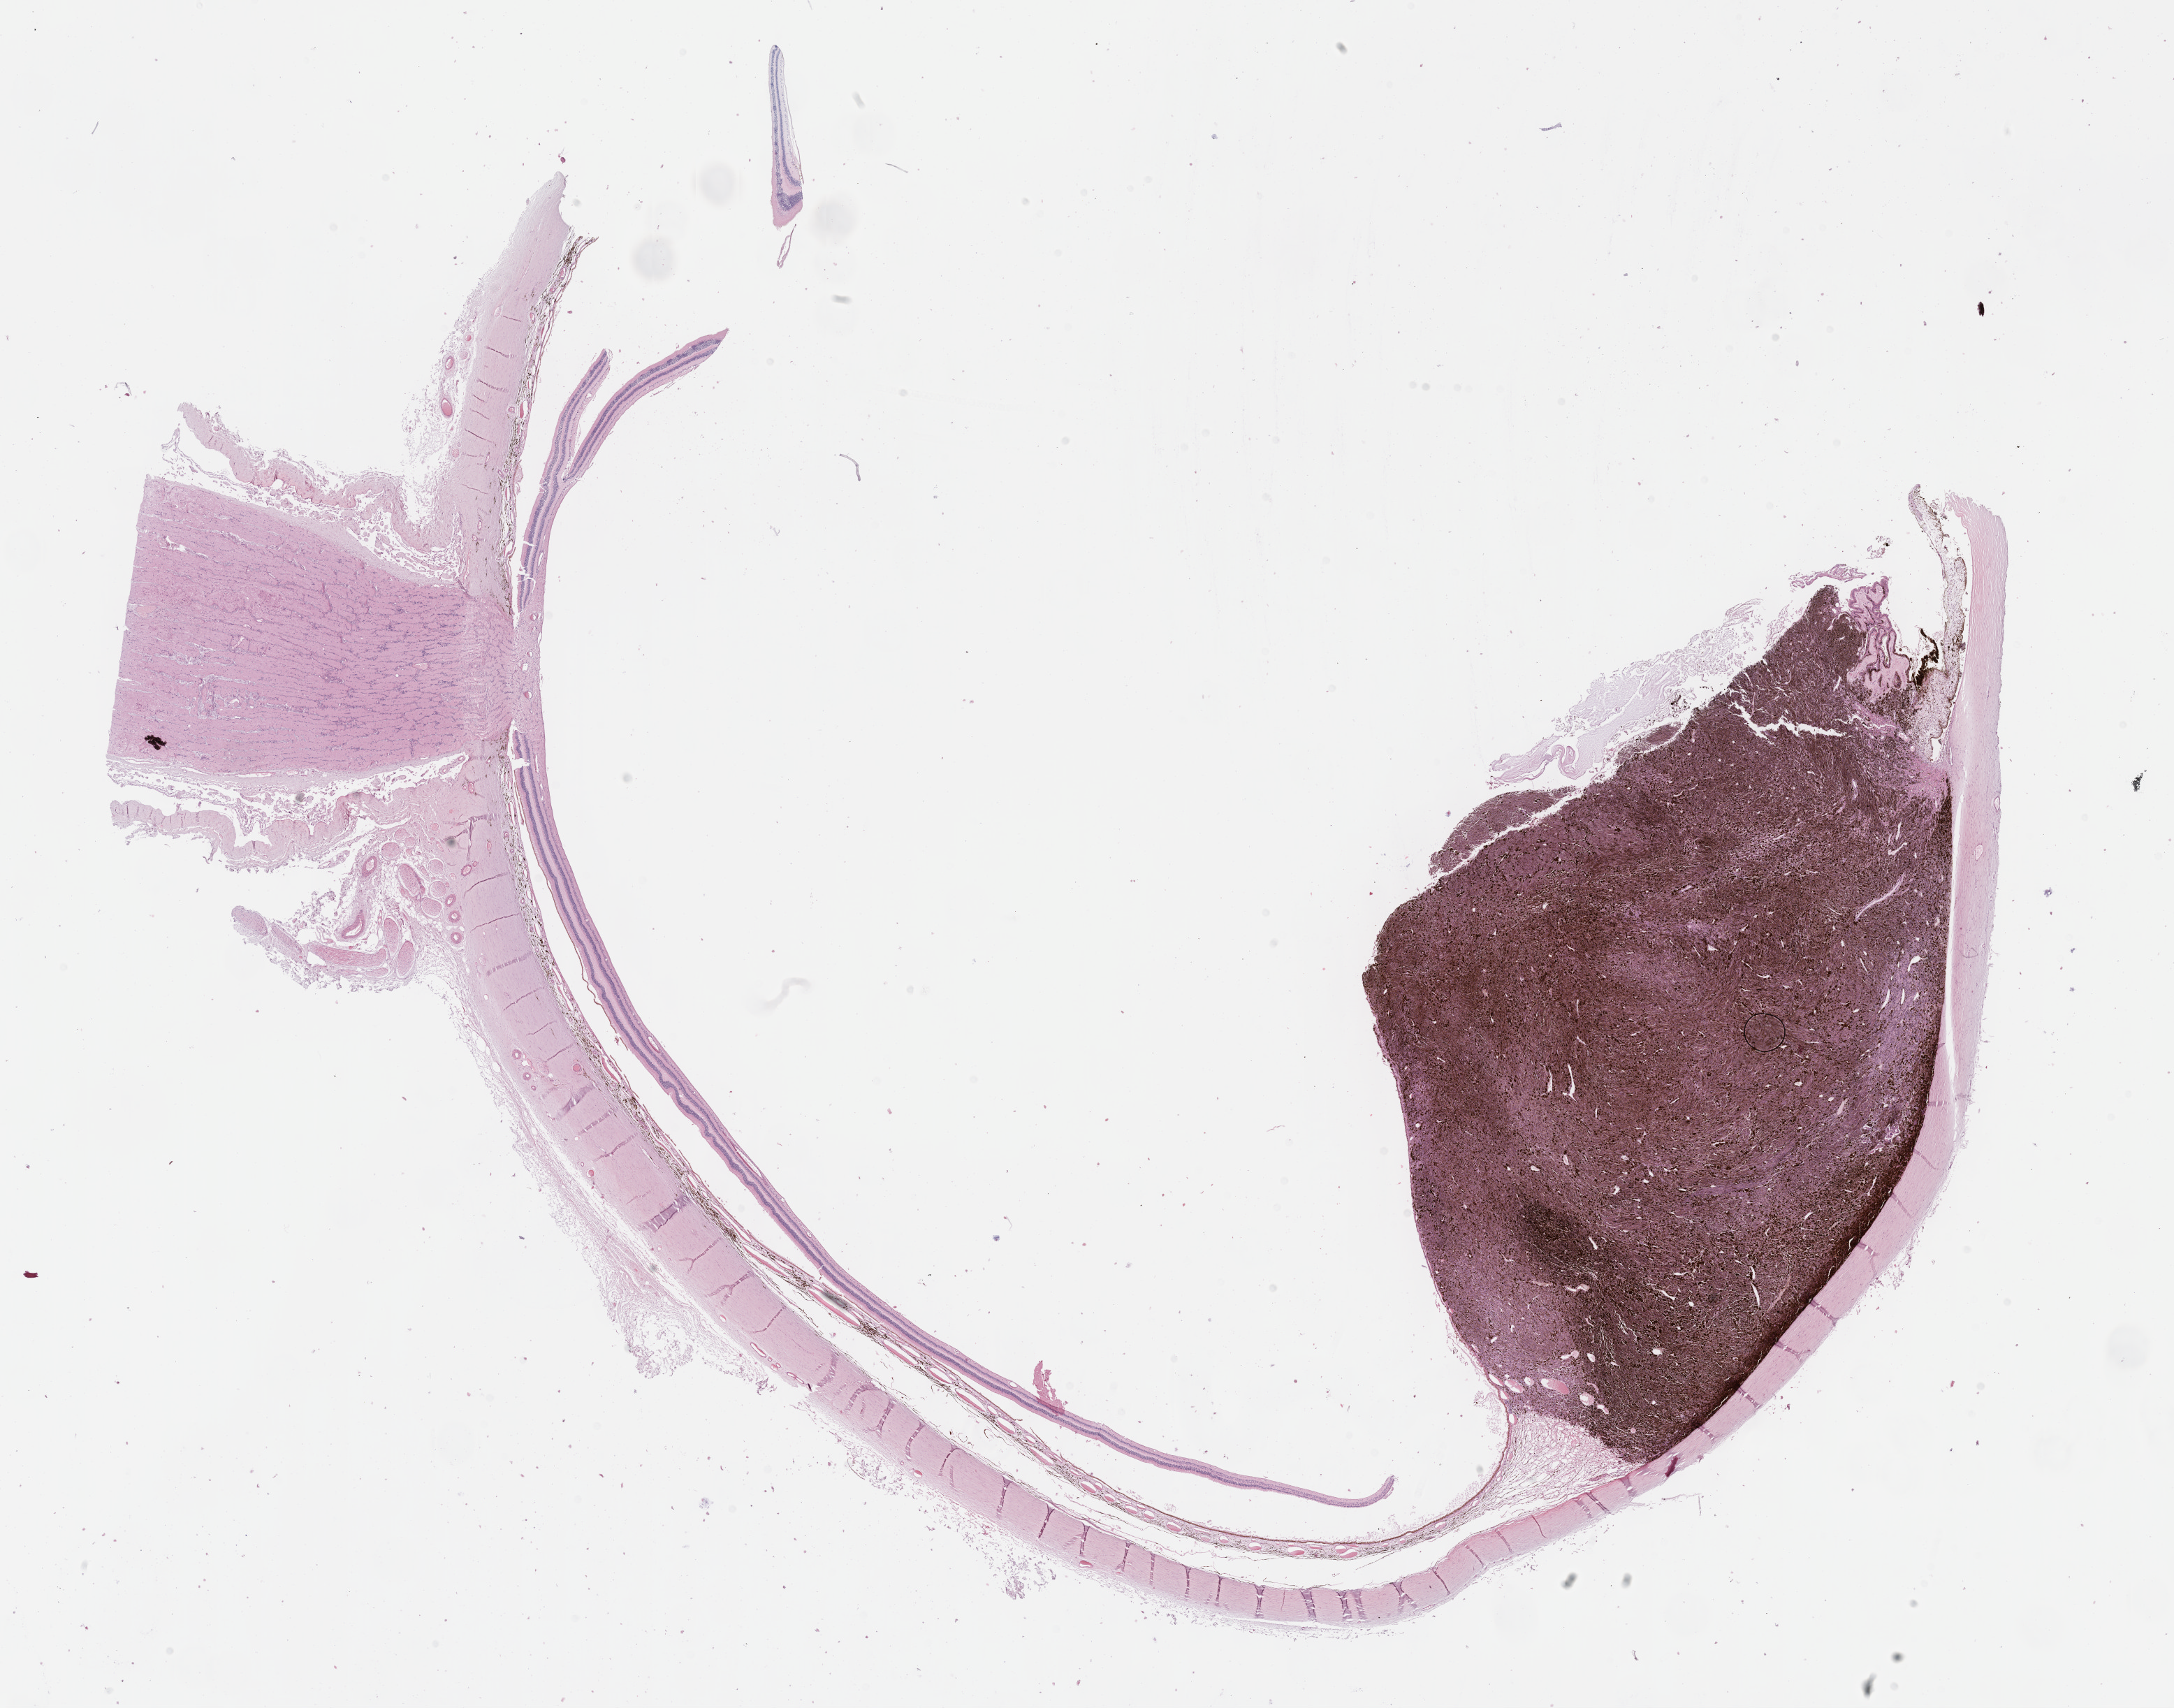
Digitized Hematoxylin and eosin (H&E) stained tissue section (whole slide) — whole scanned area (about 25.2 x 19.8 mm) shown as a low-resolution overview, FFPE section, uvea, primary tumour sample. Patient: male, age at initial diagnosis 59 years.
Diagnosis: Mixed epithelioid and spindle cell melanoma (ciliary body). Laterality: left. AJCC pathologic stage: IIIB.